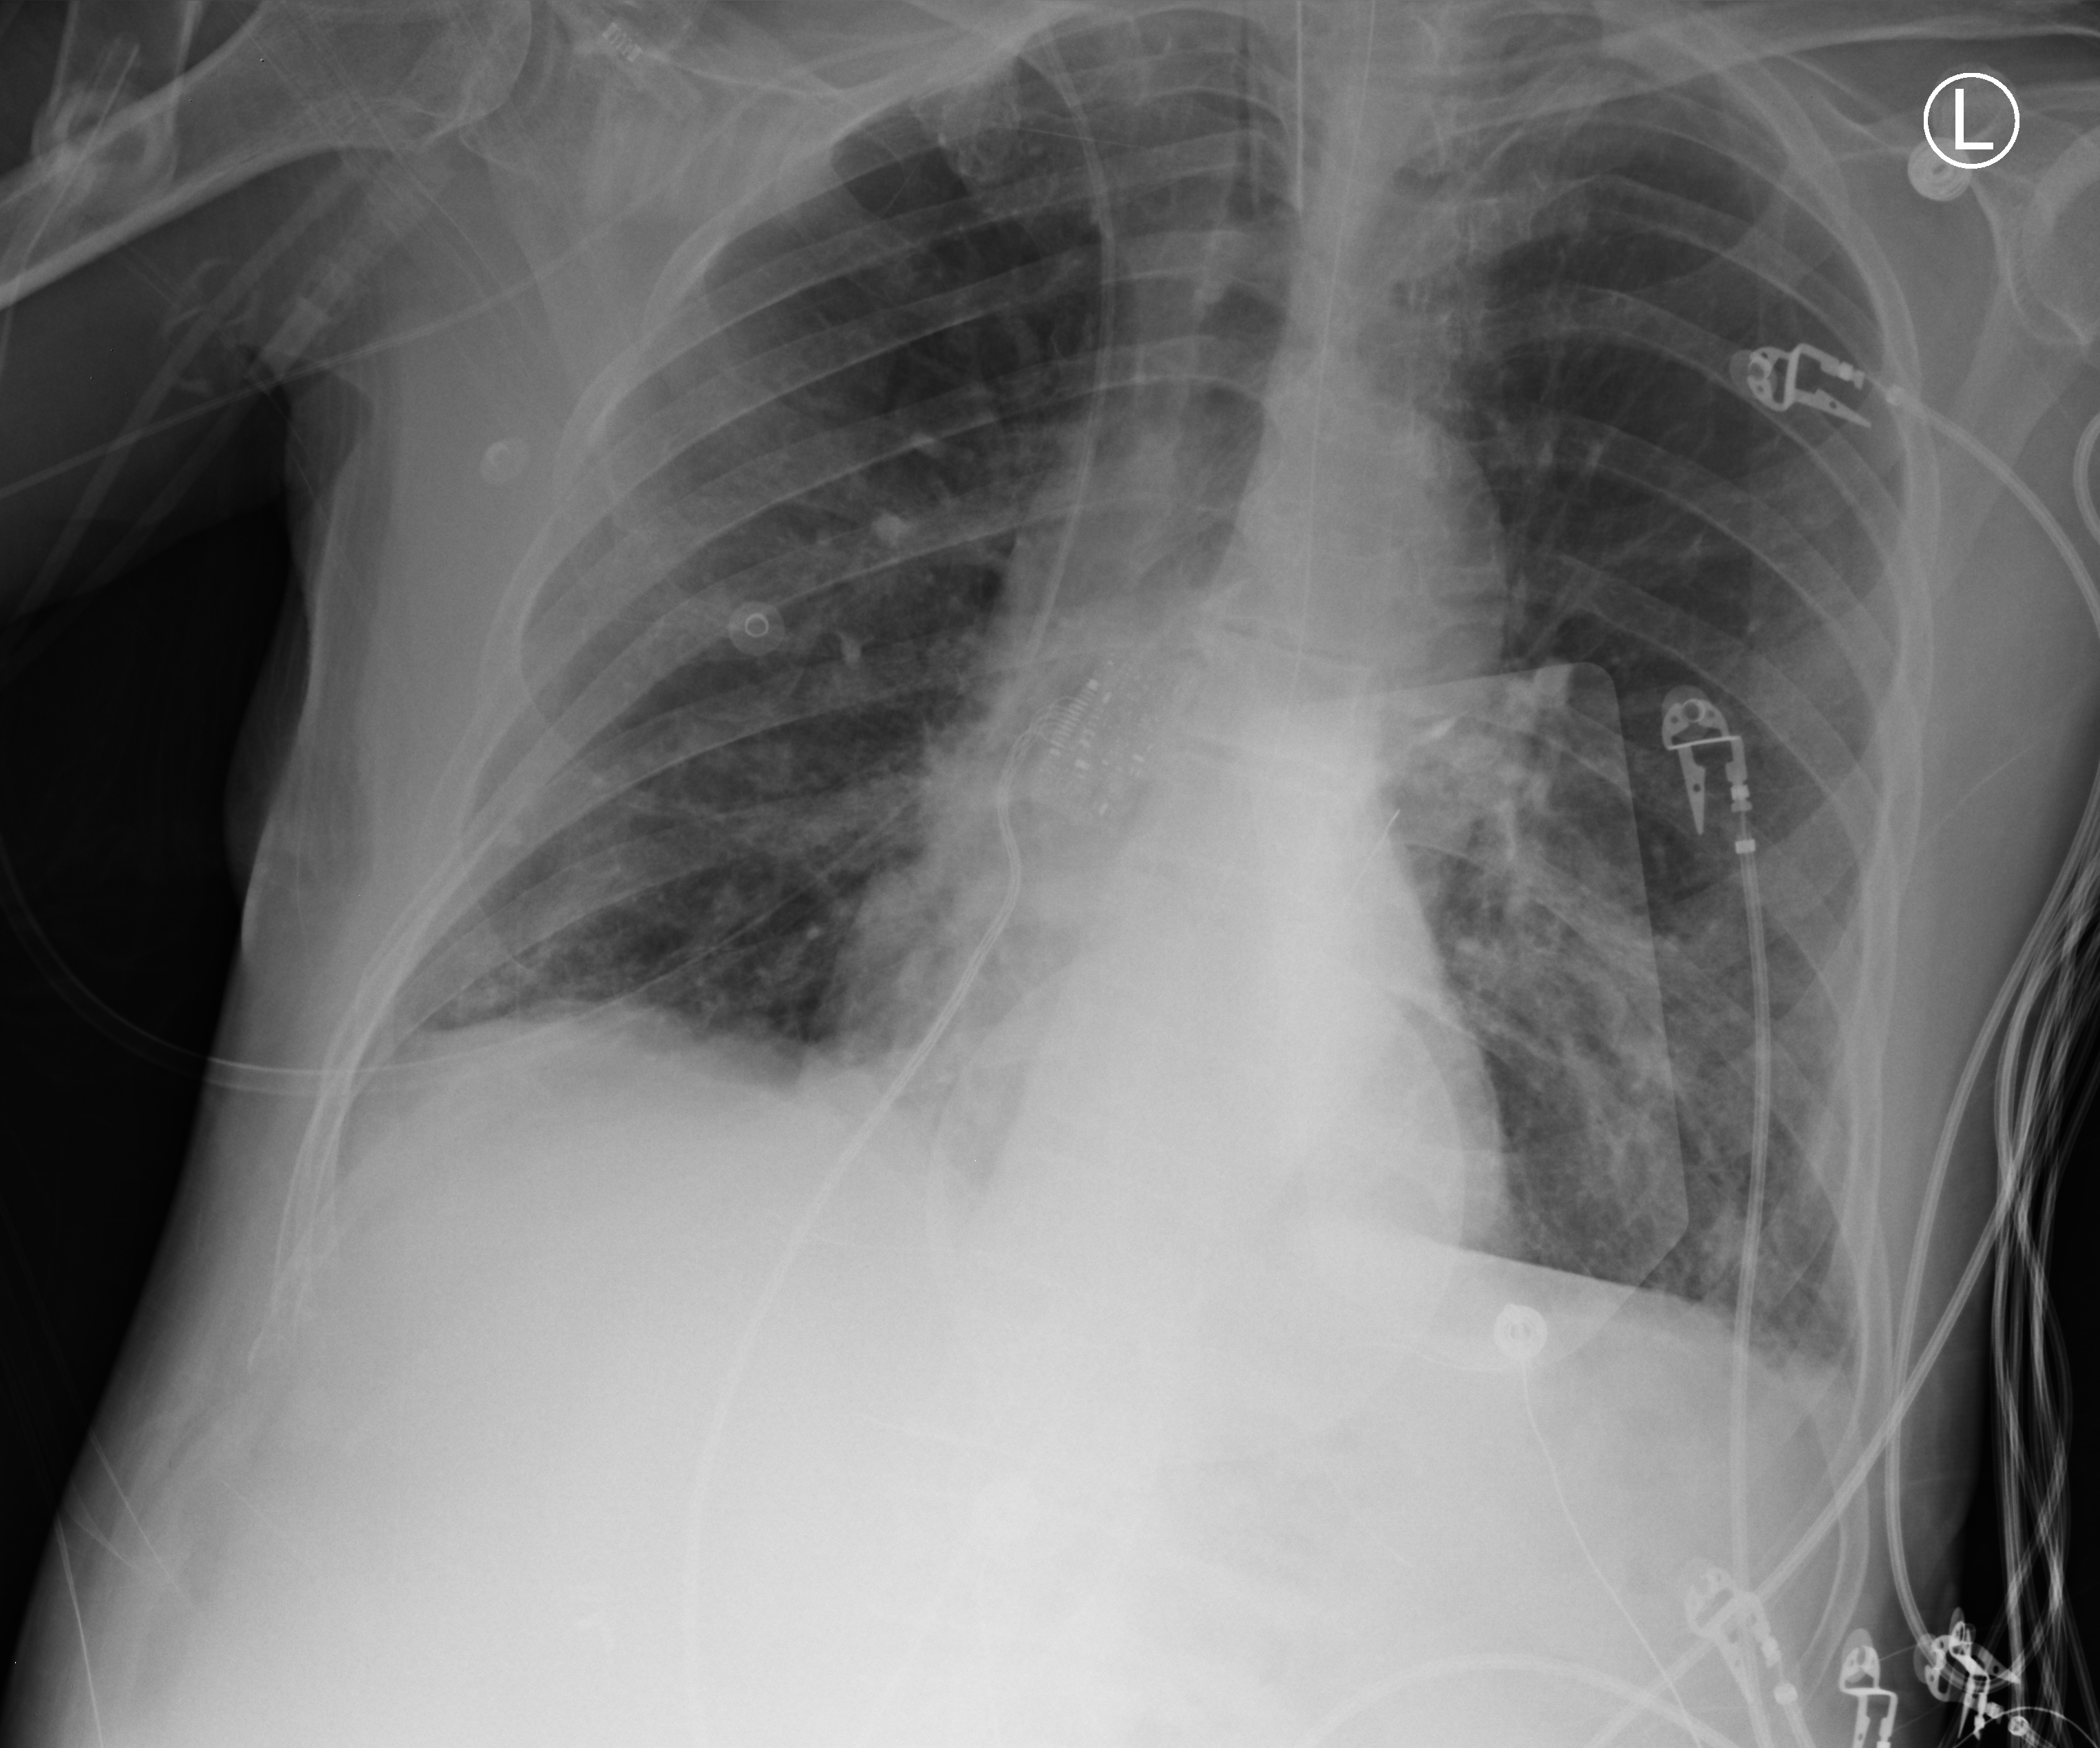
Chest X-ray (portable), anteroposterior (AP) projection. Male patient hospitalised with COVID-19, age 75–90 years.
Admission-level facts for this patient (not findings on this image; timing relative to this image not recorded): admitted to intensive care during this hospital stay: yes.